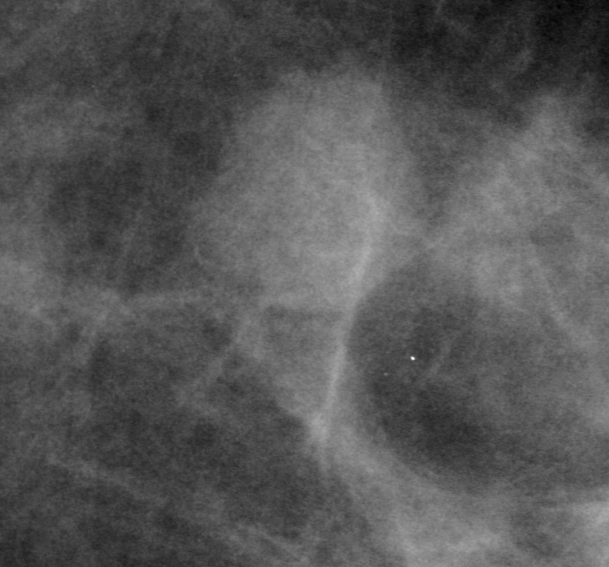
Crop from a digitized film mammogram around one marked abnormality; left breast; CC view; BI-RADS breast density category 2 (scale 1–4).
Mass, shape oval, margins microlobulated; BI-RADS assessment category 0 (incomplete: needs additional imaging); subtlety rating 4 on a 1 (subtle) to 5 (obvious) scale; pathology result (as recorded, not read from the image): benign.